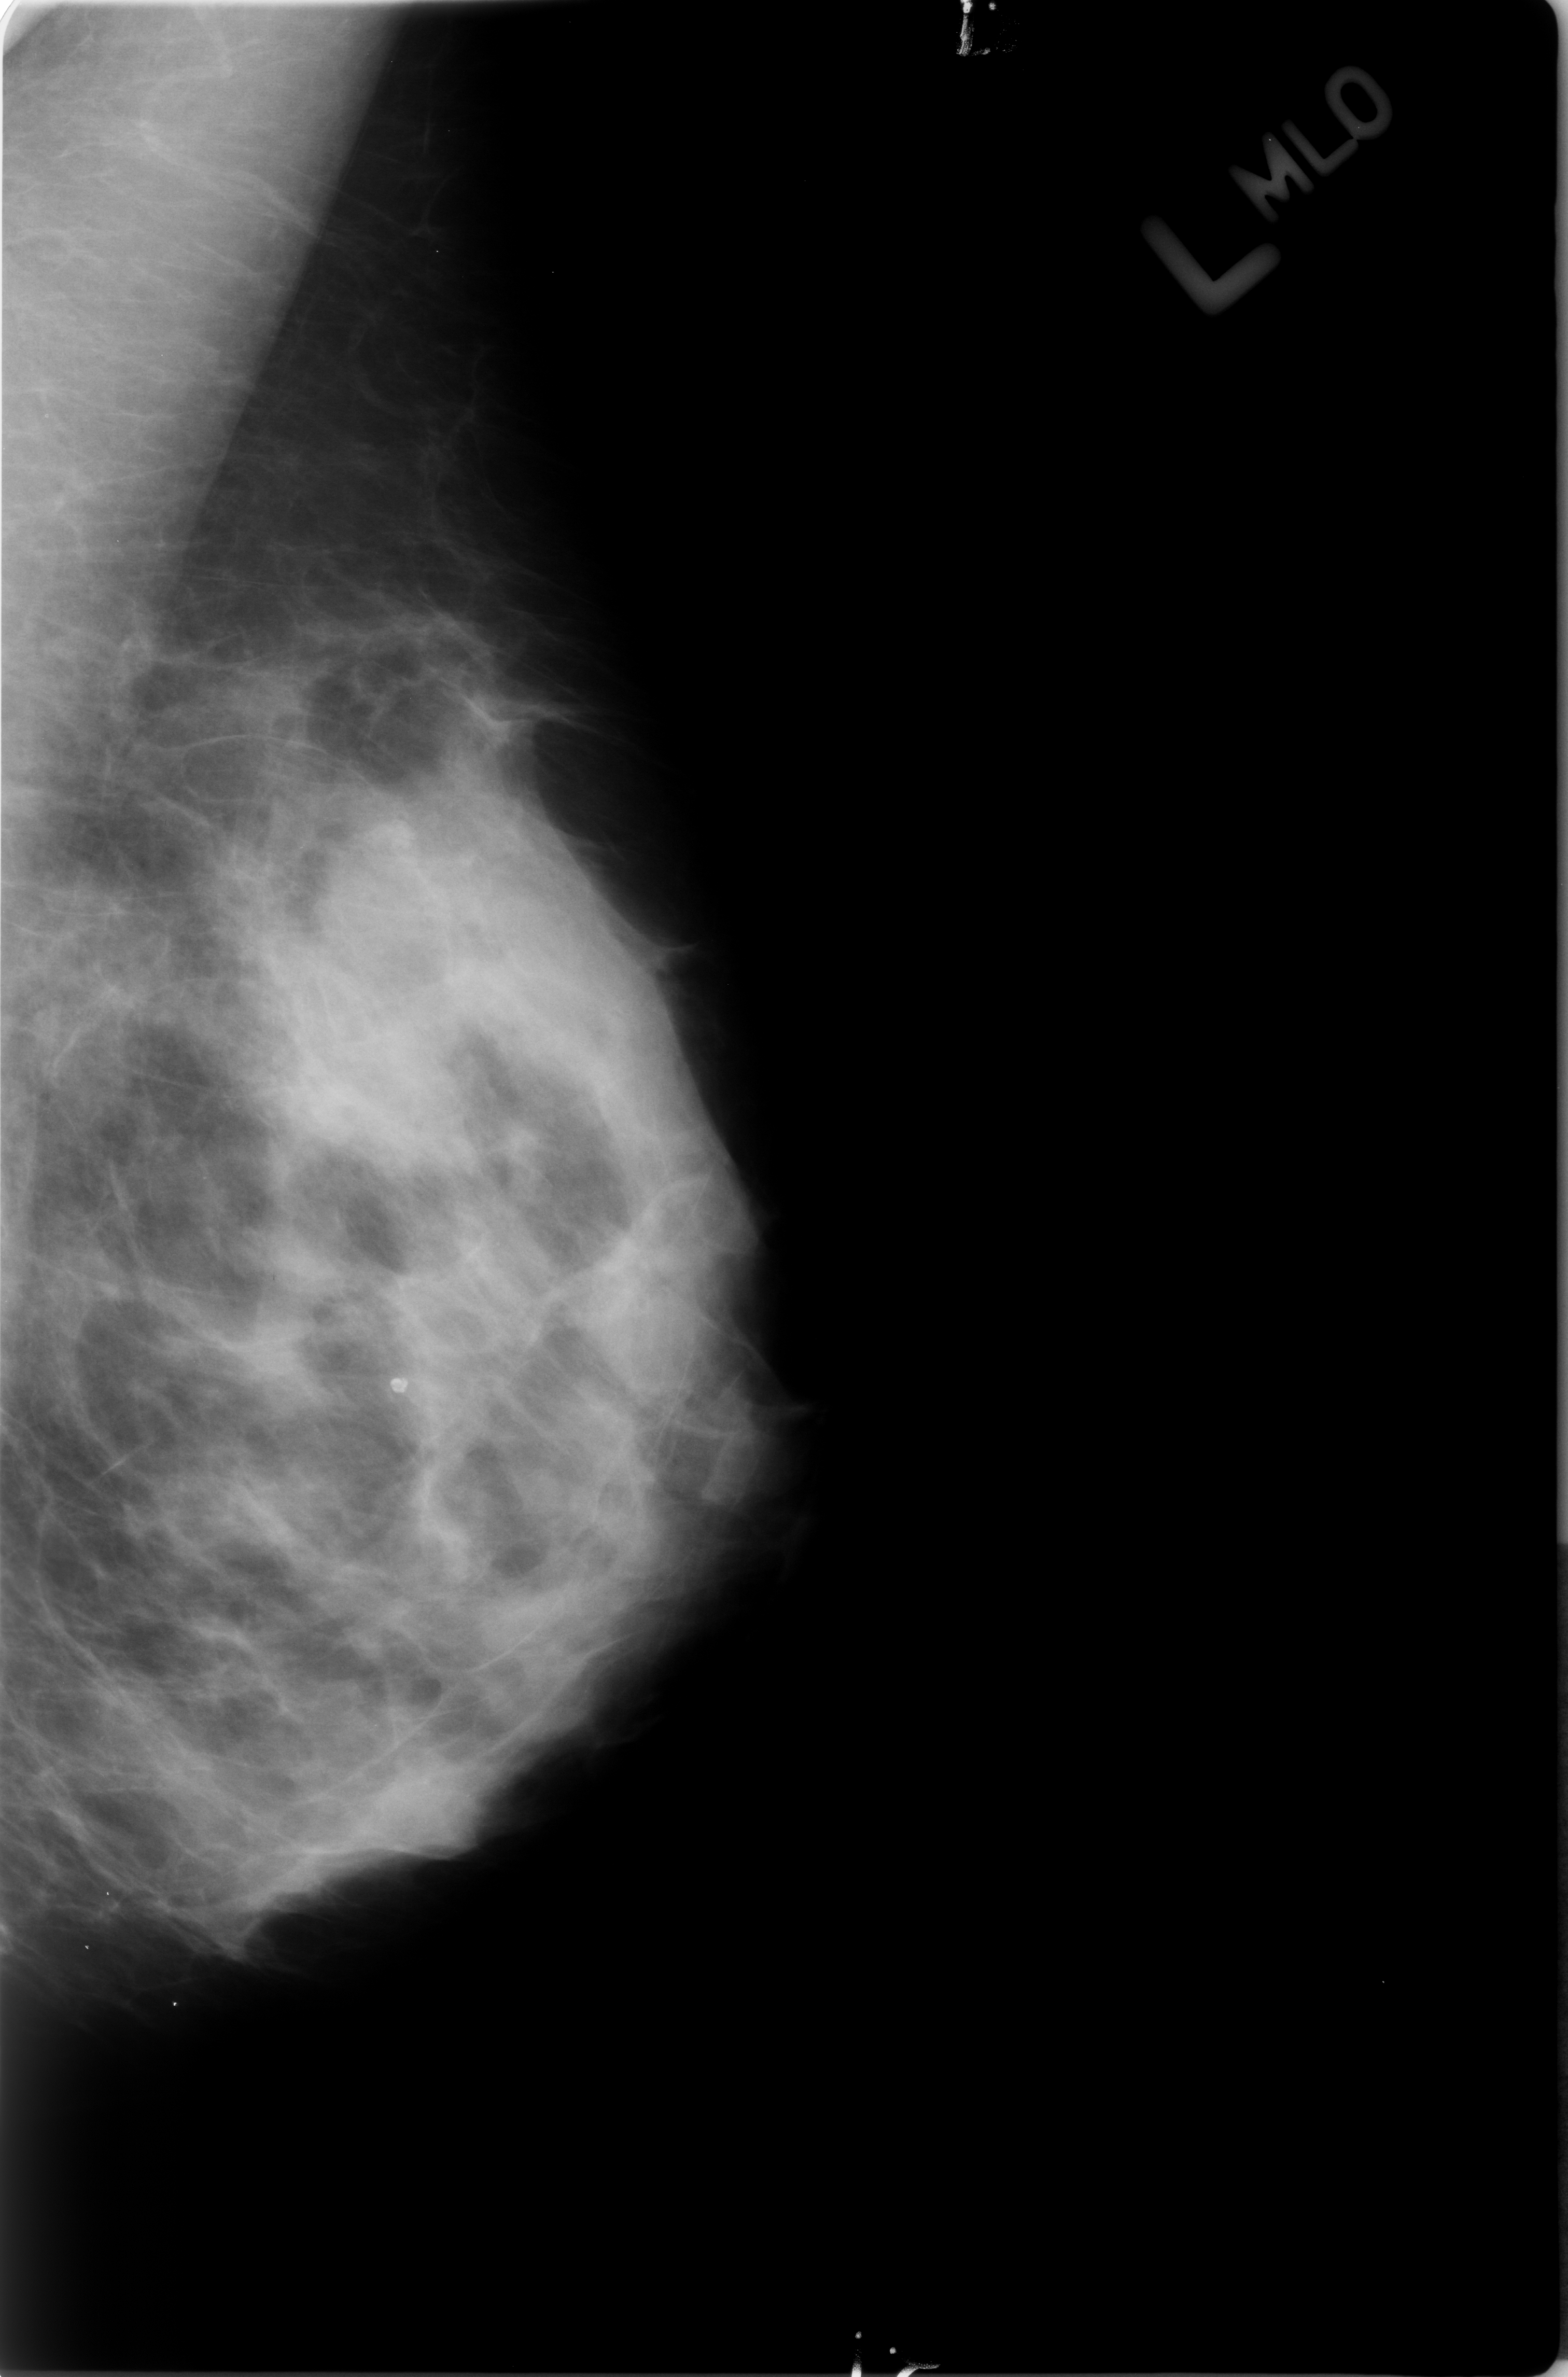
Scanned film-screen mammogram, left breast, mediolateral oblique (MLO) view, breast composition: heterogeneously dense (BI-RADS density category 3 of 4).
Marked findings (only marked abnormalities are described; nothing is implied about the rest of the image): calcifications, morphology lucent center; BI-RADS assessment category 2; benign; no additional work-up was recommended (benign without callback).